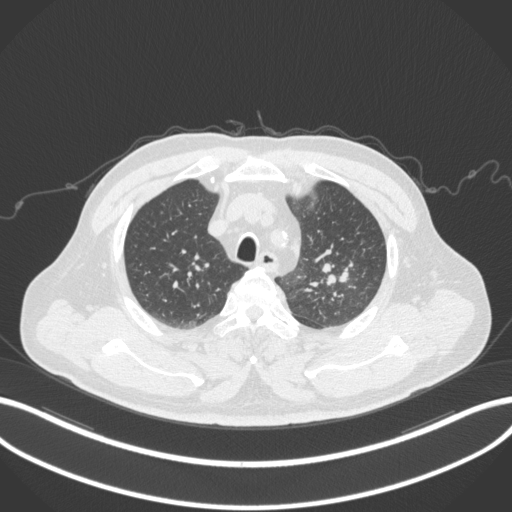
Chest CT, one axial slice; slice 242 of 286 in the series (ordered by position); reconstruction kernel B31f; 120 kVp; lung window (W 1500 / L -600 HU); 1 mm slice thickness; 512 × 512 image matrix. Male patient, age 67 years. Case-level facts recorded for this patient, not image findings: clinical TNM (as recorded): T2a N1 M0; histopathological grade: G3.
Structures marked on this image (bounding box drawn by a radiologist):
- lung tumour (recorded histology: adenocarcinoma): bounding box [x1, y1, x2, y2] px = [322, 259, 350, 286]